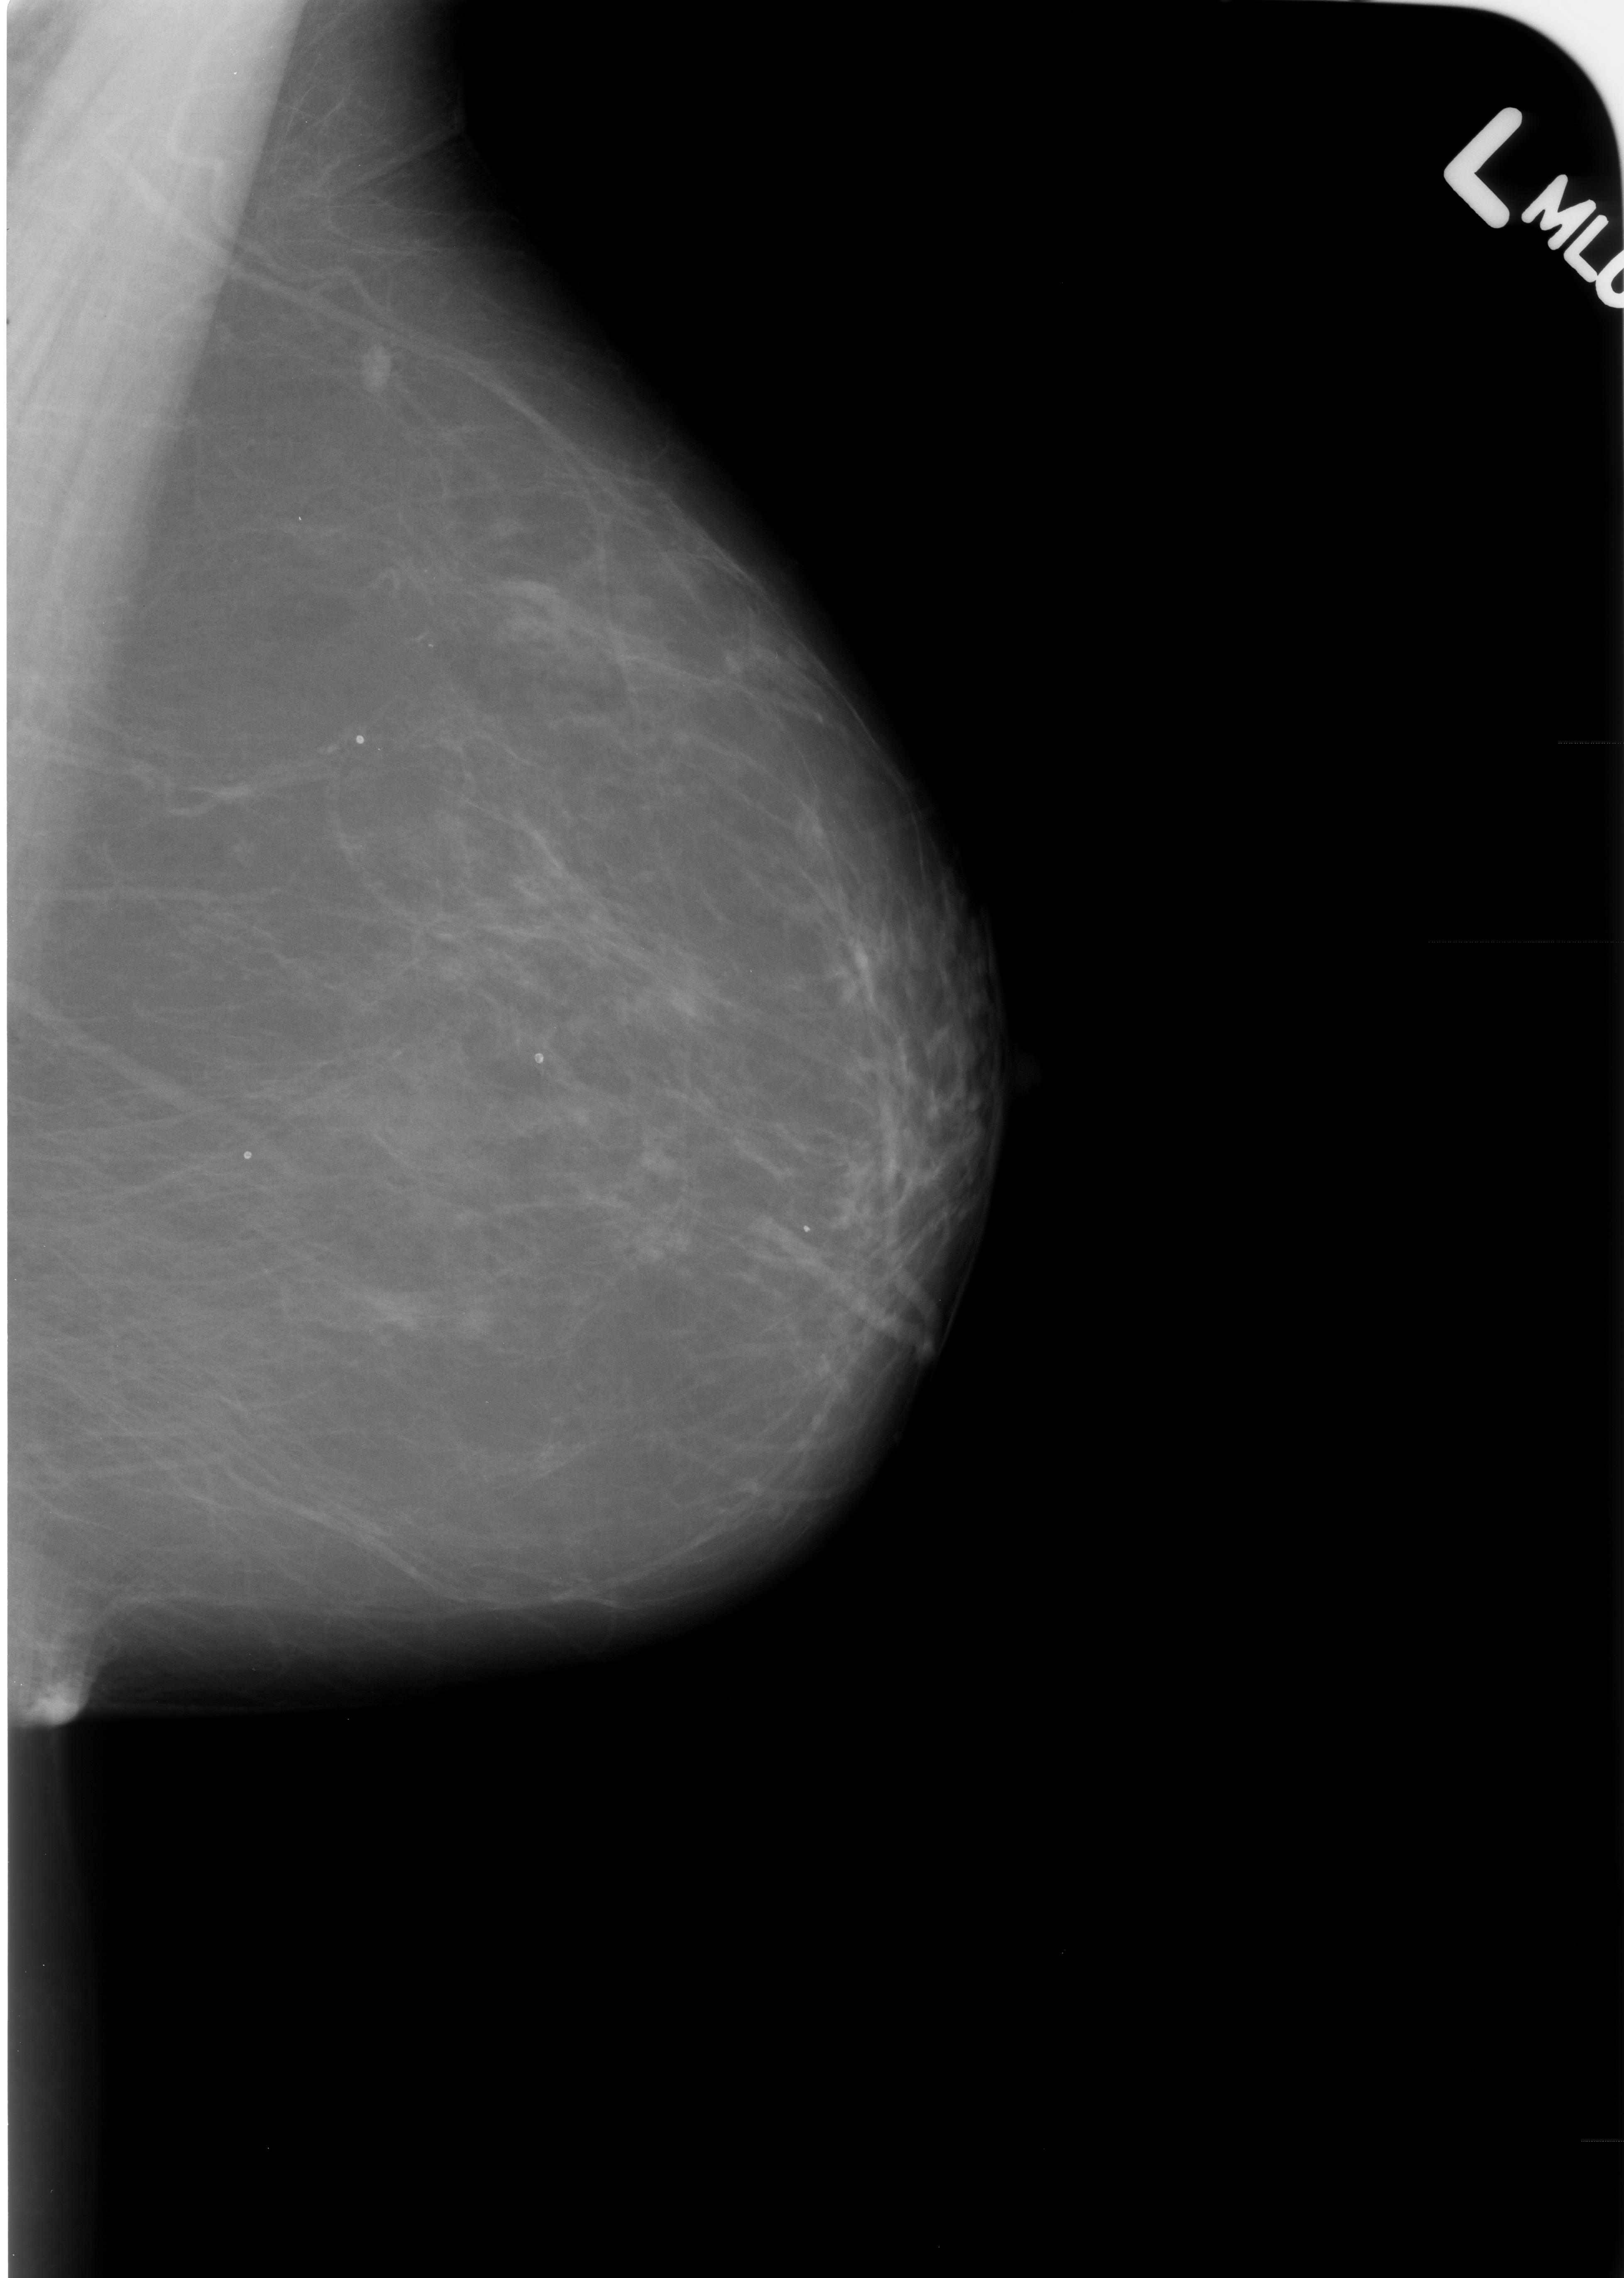
Digitized screen-film mammogram, left breast, mediolateral oblique (MLO) view.
Radiologist-marked abnormalities on this image: Finding 1 of 4: calcifications, morphology lucent centered; BI-RADS assessment category 2; subtlety rating 3 on a 1 (subtle) to 5 (obvious) scale; benign; no additional work-up was recommended (benign without callback). Finding 2 of 4: calcifications, morphology lucent centered; BI-RADS assessment category 2; benign without callback (not worked up further). Finding 3 of 4: calcifications, morphology lucent centered; BI-RADS assessment category 2; benign without callback (not worked up further). Finding 4 of 4: calcifications, morphology lucent centered; BI-RADS assessment category 2; subtlety rating 3 on a 1 (subtle) to 5 (obvious) scale; benign; no additional work-up was recommended (benign without callback).